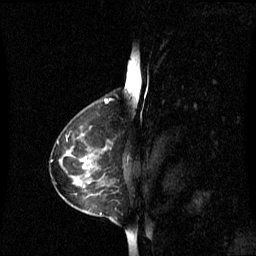
Breast MRI (dynamic contrast-enhanced), one sagittal slice; position 39 of 60 along the scan axis; dynamic contrast-enhanced series, image 2 of 3 at this slice position (ordered by acquisition); 1.5 T; TE 4.2 ms, TR 8.4 ms; 2.1 mm slice thickness; 256 × 256 image matrix. Female patient, age 42 years. Case-level facts recorded for this patient, not image findings: setting: breast cancer imaged before/during neoadjuvant chemotherapy; receptor status: HR-positive, HER2-negative.
Structures marked on this image (semi-automatic segmentation, software-assisted and operator-edited):
- analysis volume of interest (the breast-tissue region the enhancement analysis was run in; not a lesion): bounding box (x1, y1, x2, y2) in pixels: (60, 126, 111, 195)
- tumour enhancement mask (voxels above the 70 % enhancement threshold inside the analysis volume of interest): (80, 160, 85, 163)